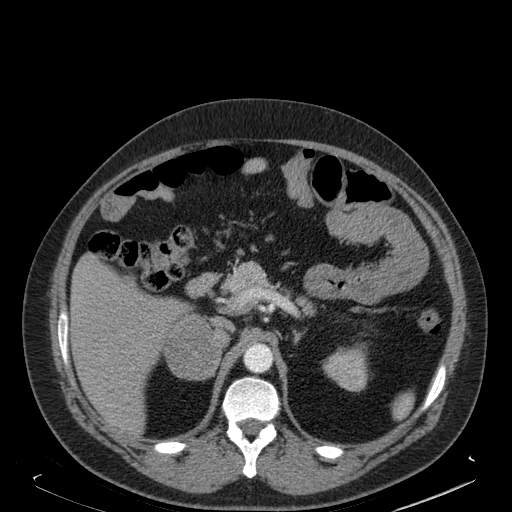
Contrast-enhanced abdominal CT, one axial slice; soft-tissue window (W 400 / L 40 HU); 1.5 mm slice thickness; 512 × 512 image matrix, field of view 405 × 405 mm. Male patient. Case-level facts recorded for this patient, not image findings: diagnosis: adrenocortical carcinoma; tumour side: right adrenal.
Outlined on this slice (semi-automatically segmented with operator editing):
- mass: bounding box (x1, y1, x2, y2) in pixels: (167, 318, 221, 379)